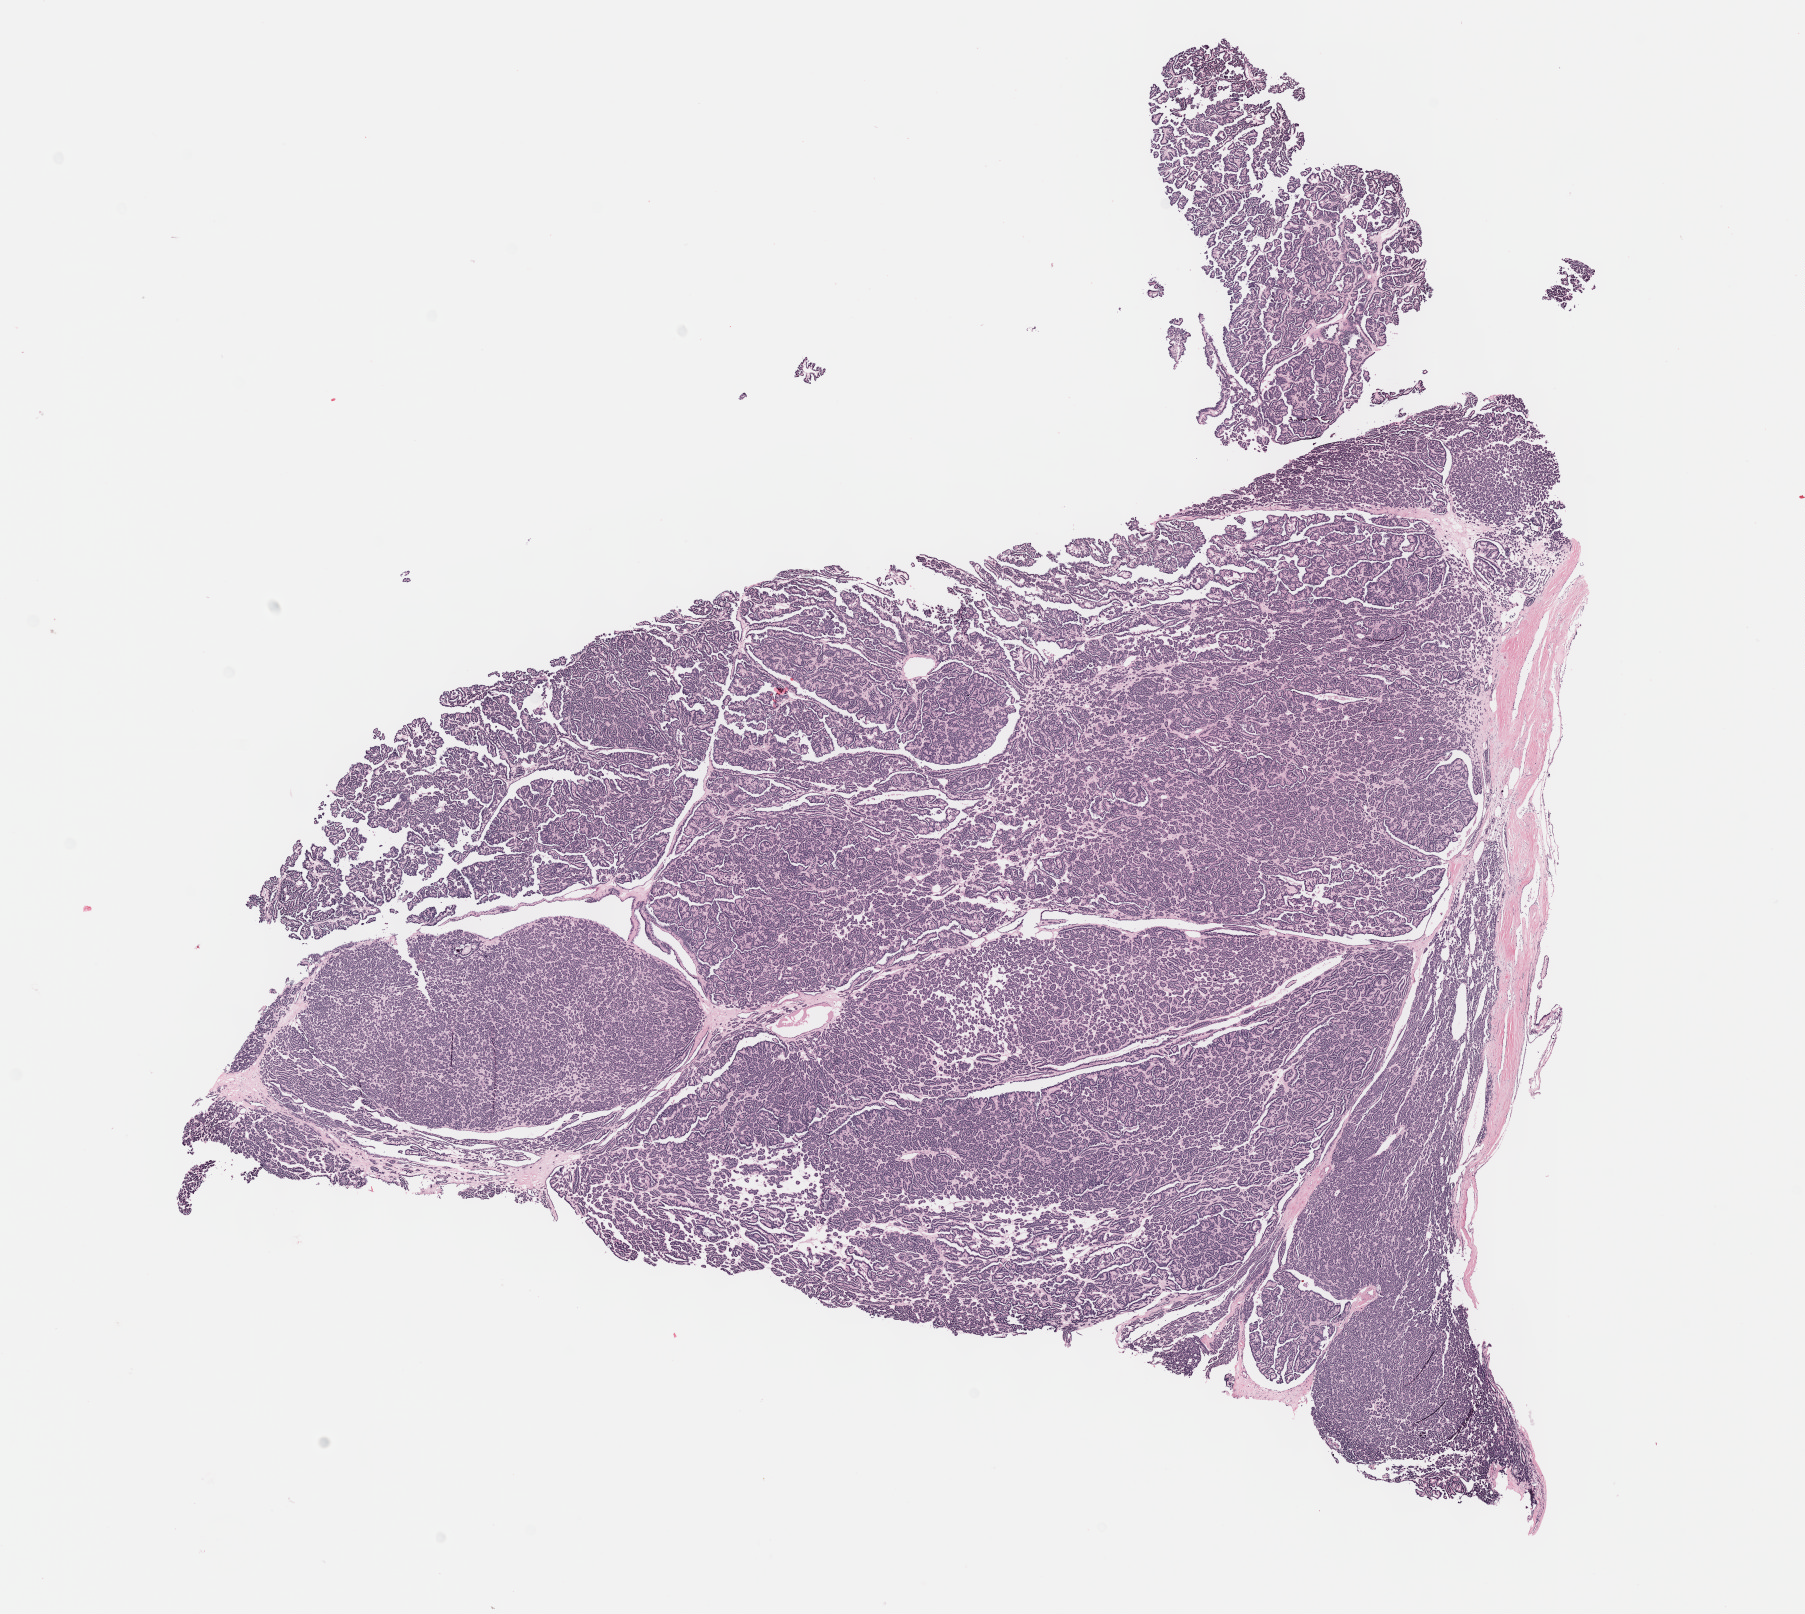
Digitized H&E tissue section (whole slide), a low-resolution overview of the entire scanned area, about 14.6 x 13.1 mm (from a 40x scan), formalin-fixed paraffin-embedded (FFPE) diagnostic section, sample: primary tumour, kidney. Female, age 54 years at initial diagnosis.
Diagnosis: Papillary adenocarcinoma, NOS.